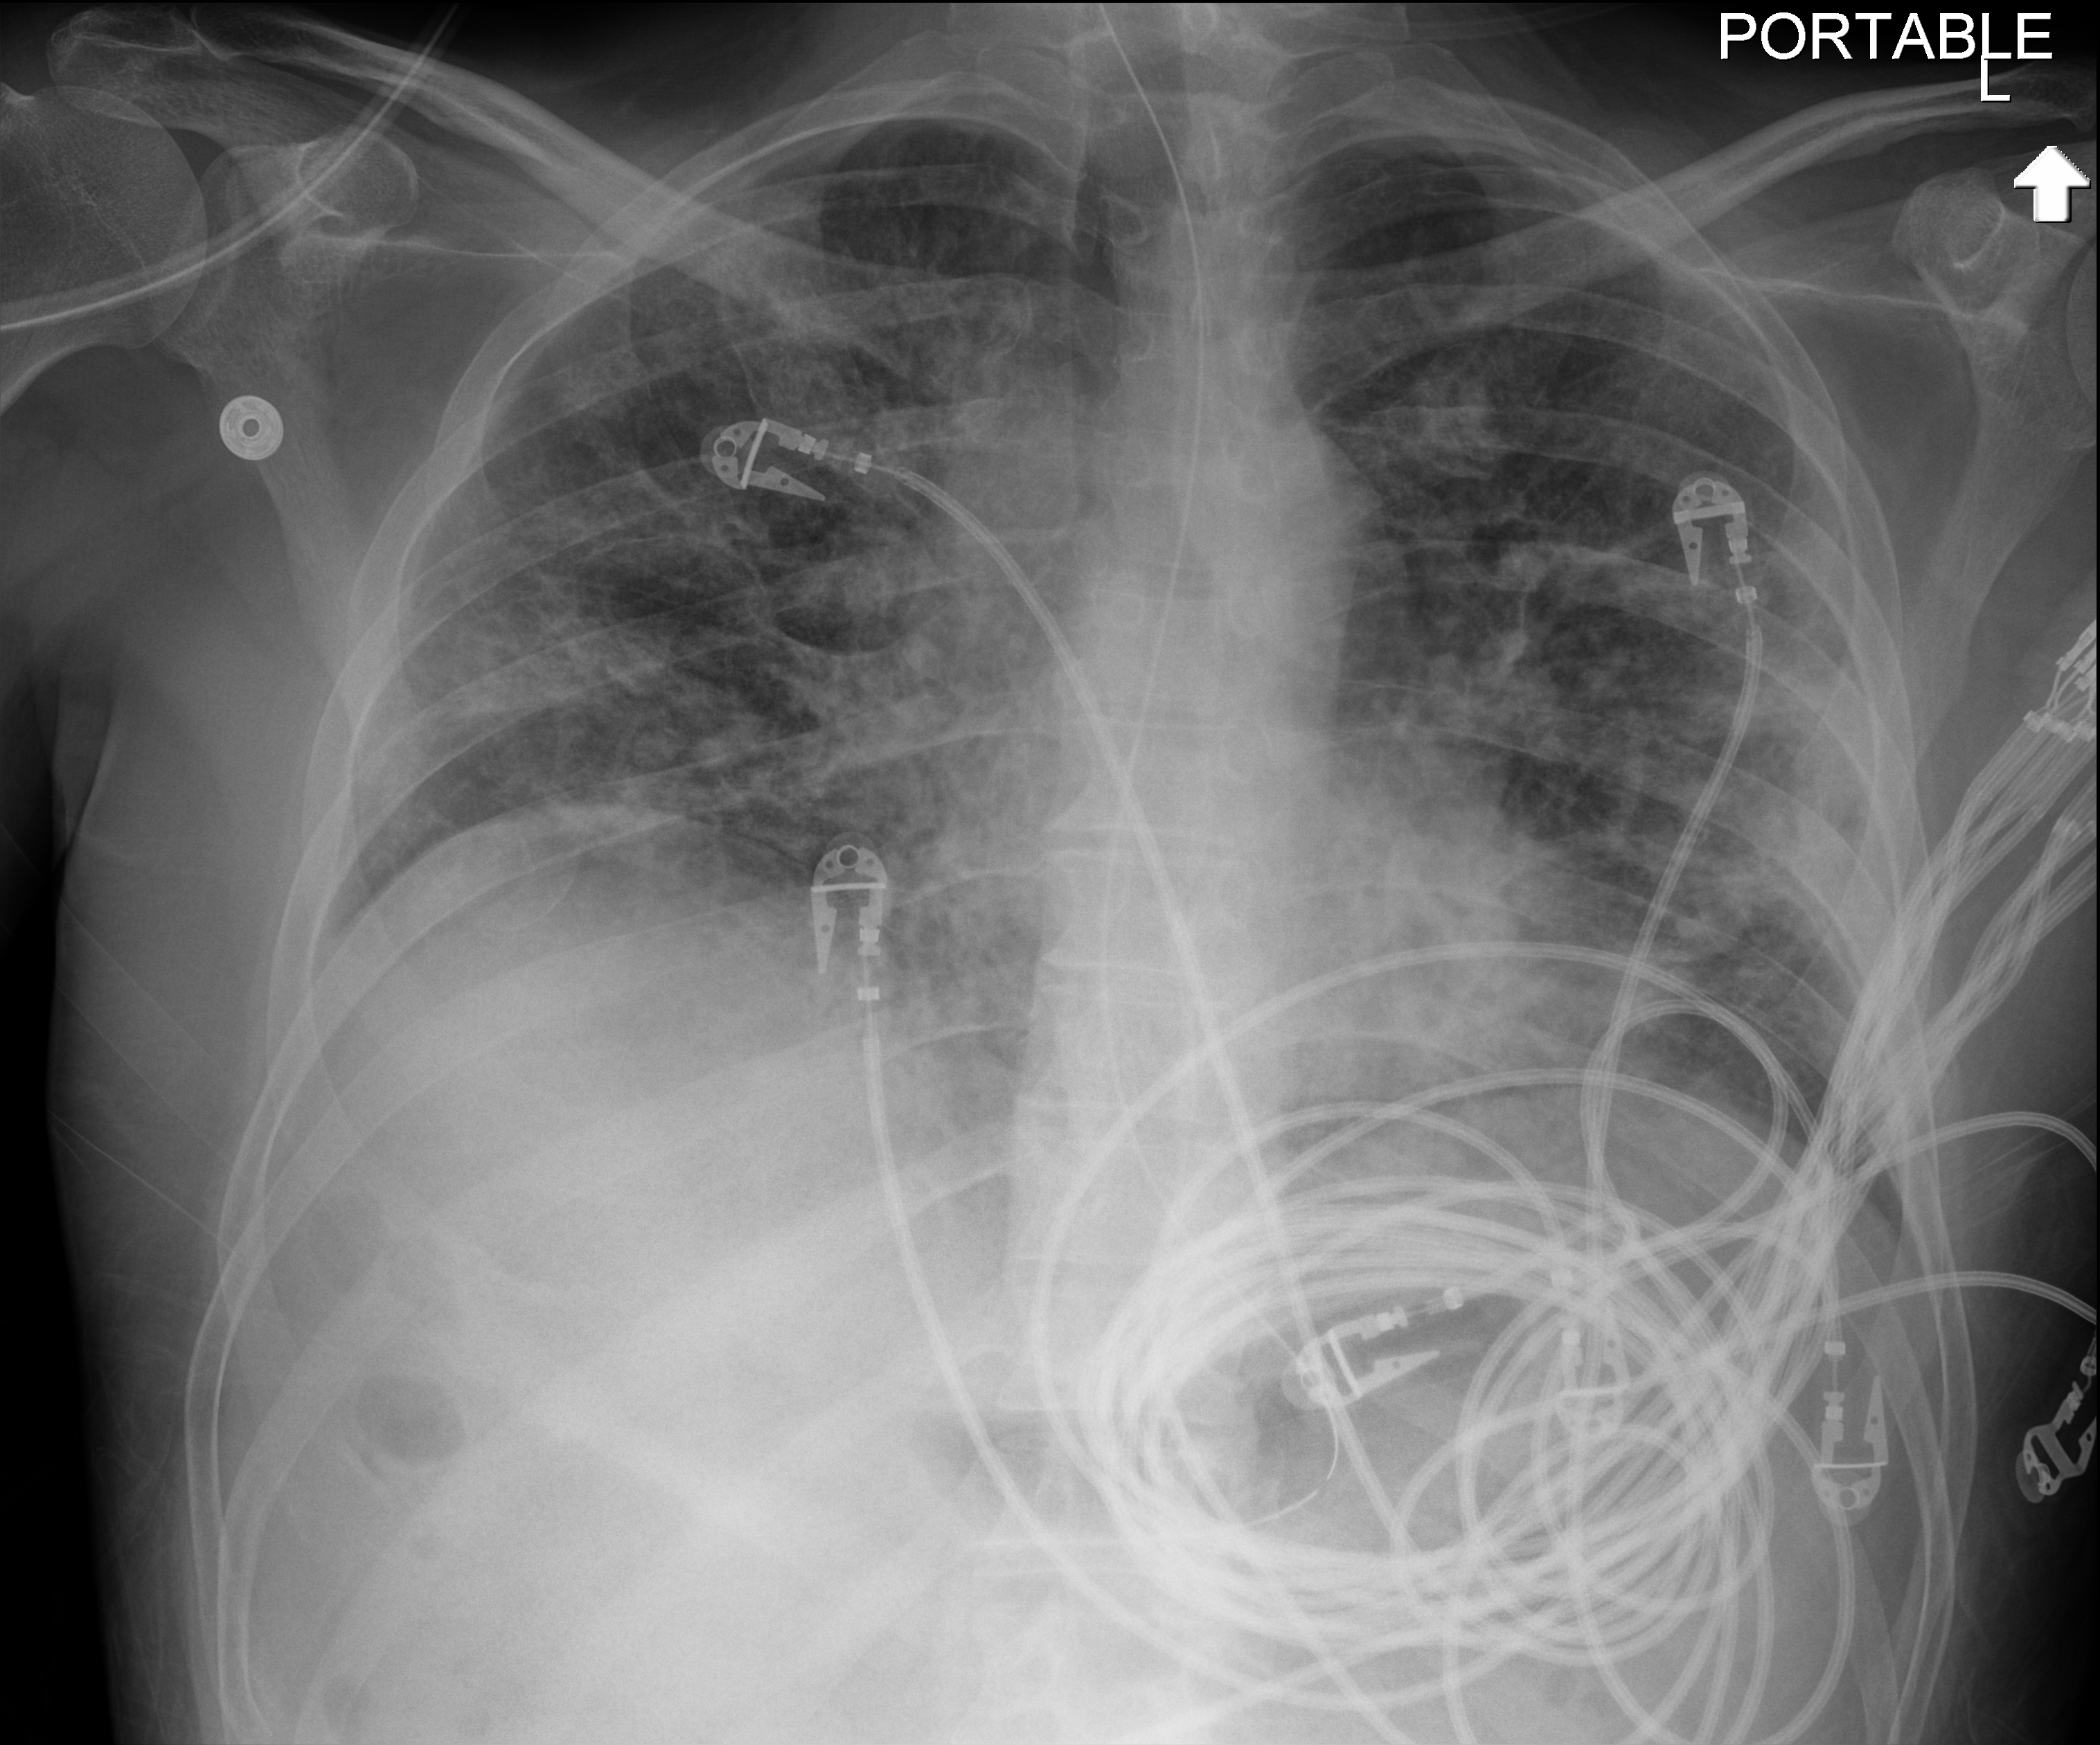
Bedside chest radiograph (digital radiography); anteroposterior (AP) projection. Patient hospitalised with COVID-19; male, aged 18–59 years.
Admission-level facts for this patient (not findings on this image; timing relative to this image not recorded): mechanically ventilated during this hospital stay: yes.